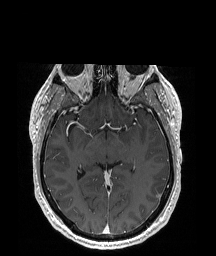
Brain MRI from a brain-tumour surgery series, one axial slice; slice 110 of 192 in the series (ordered by position); T1-weighted post-contrast; 1 mm slice thickness; 216 × 256 image matrix, field of view 219 × 260 mm. From the clinical record (not read from this slice): histopathology: Glioblastoma; WHO grade: 4; IDH mutation: no.
Outlined on this slice (outlined manually by an expert reader):
- tumour: bounding box [x1, y1, x2, y2] px = [150, 176, 161, 197]